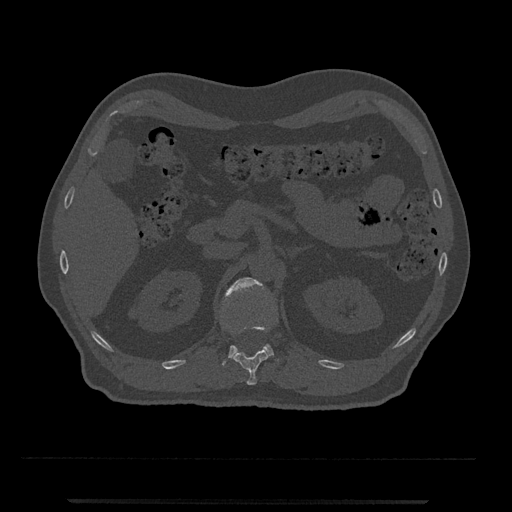
CT including the spine, one axial slice; position 373 of 797 along the scan axis; reconstruction kernel Br40s/3; 120 kVp; bone window (W 1800 / L 400 HU); 512 × 512 image matrix, field of view 419 × 419 mm. Male patient, age 63 years. From the clinical record (not read from this slice): primary cancer: prostate.
Annotated regions visible in this slice (semi-automatically segmented with operator editing):
- L1 vertebra: bounding box [x1, y1, x2, y2] px = [222, 277, 280, 366]
- T12 vertebra: [231, 324, 269, 385]